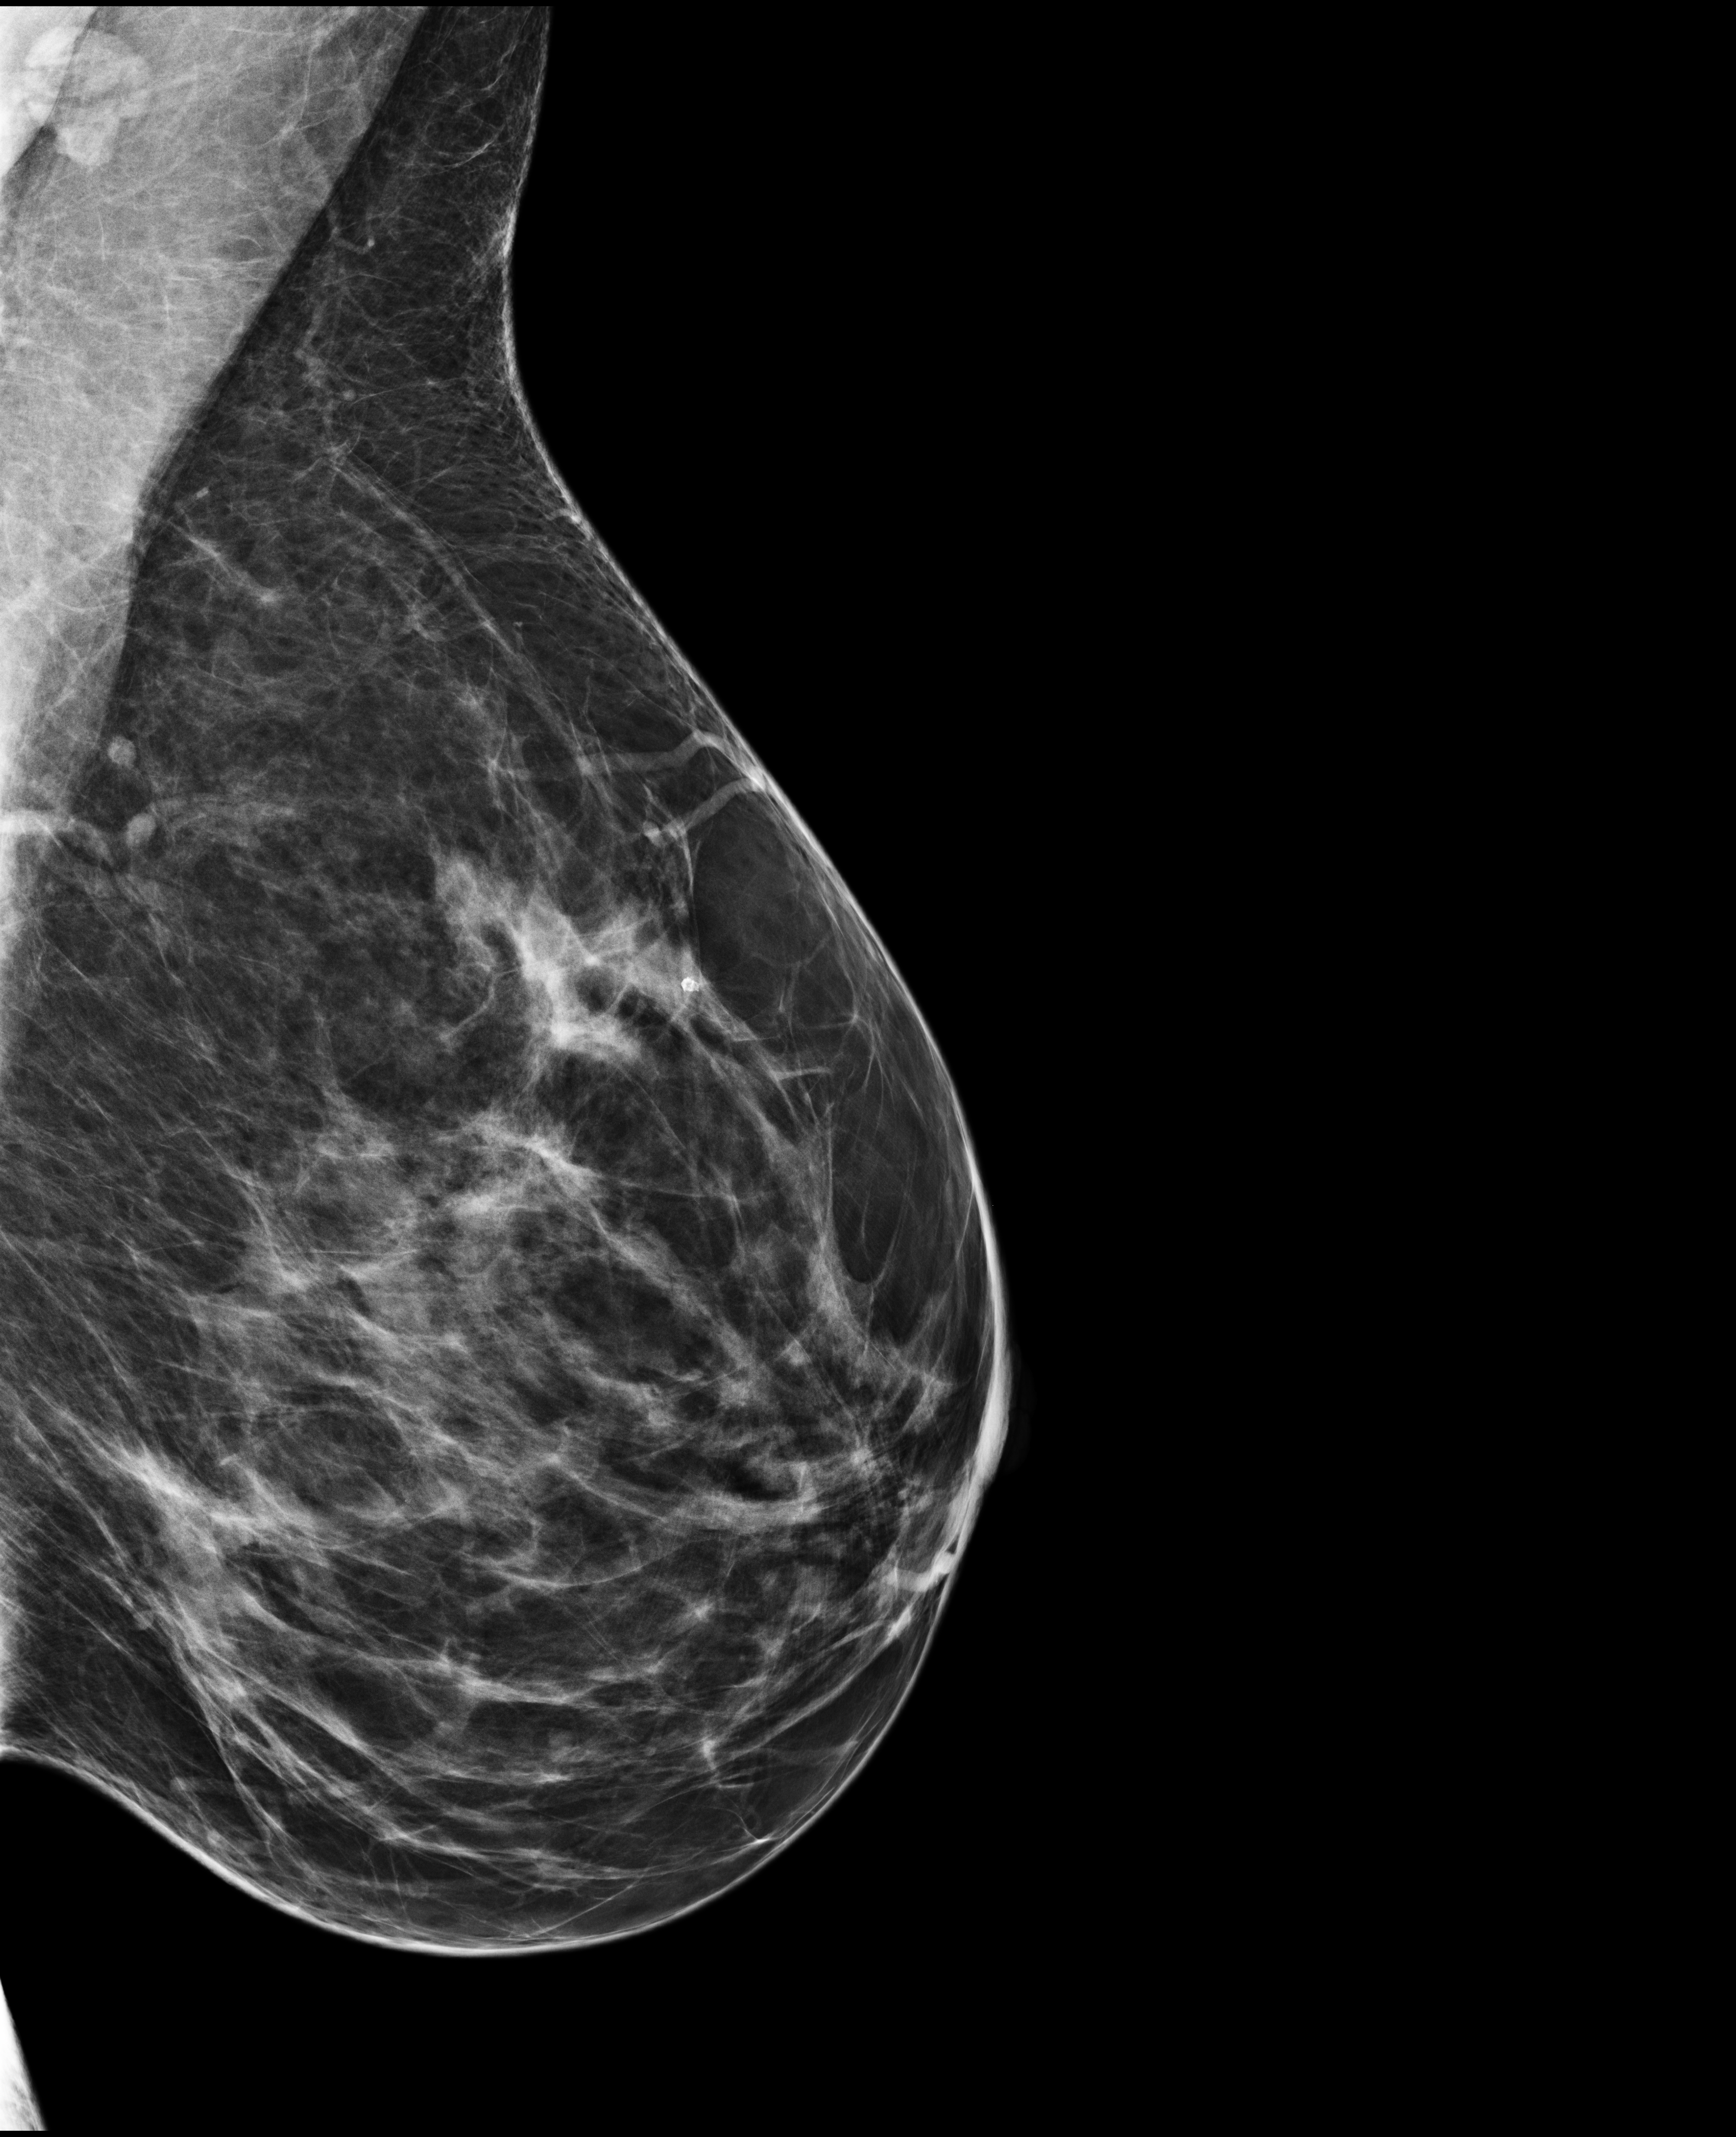
Full-field digital mammogram (FFDM), left breast, mediolateral oblique (MLO) view, annual screening mammography examination, compressed breast thickness 78 mm. Patient: female, 47 years.
- breast density at the screening exam (both breasts): heterogeneously dense (BI-RADS density category c)
- final BI-RADS category for the screening round (tomosynthesis exam, both breasts): category 2
- recall: no recall after this screen